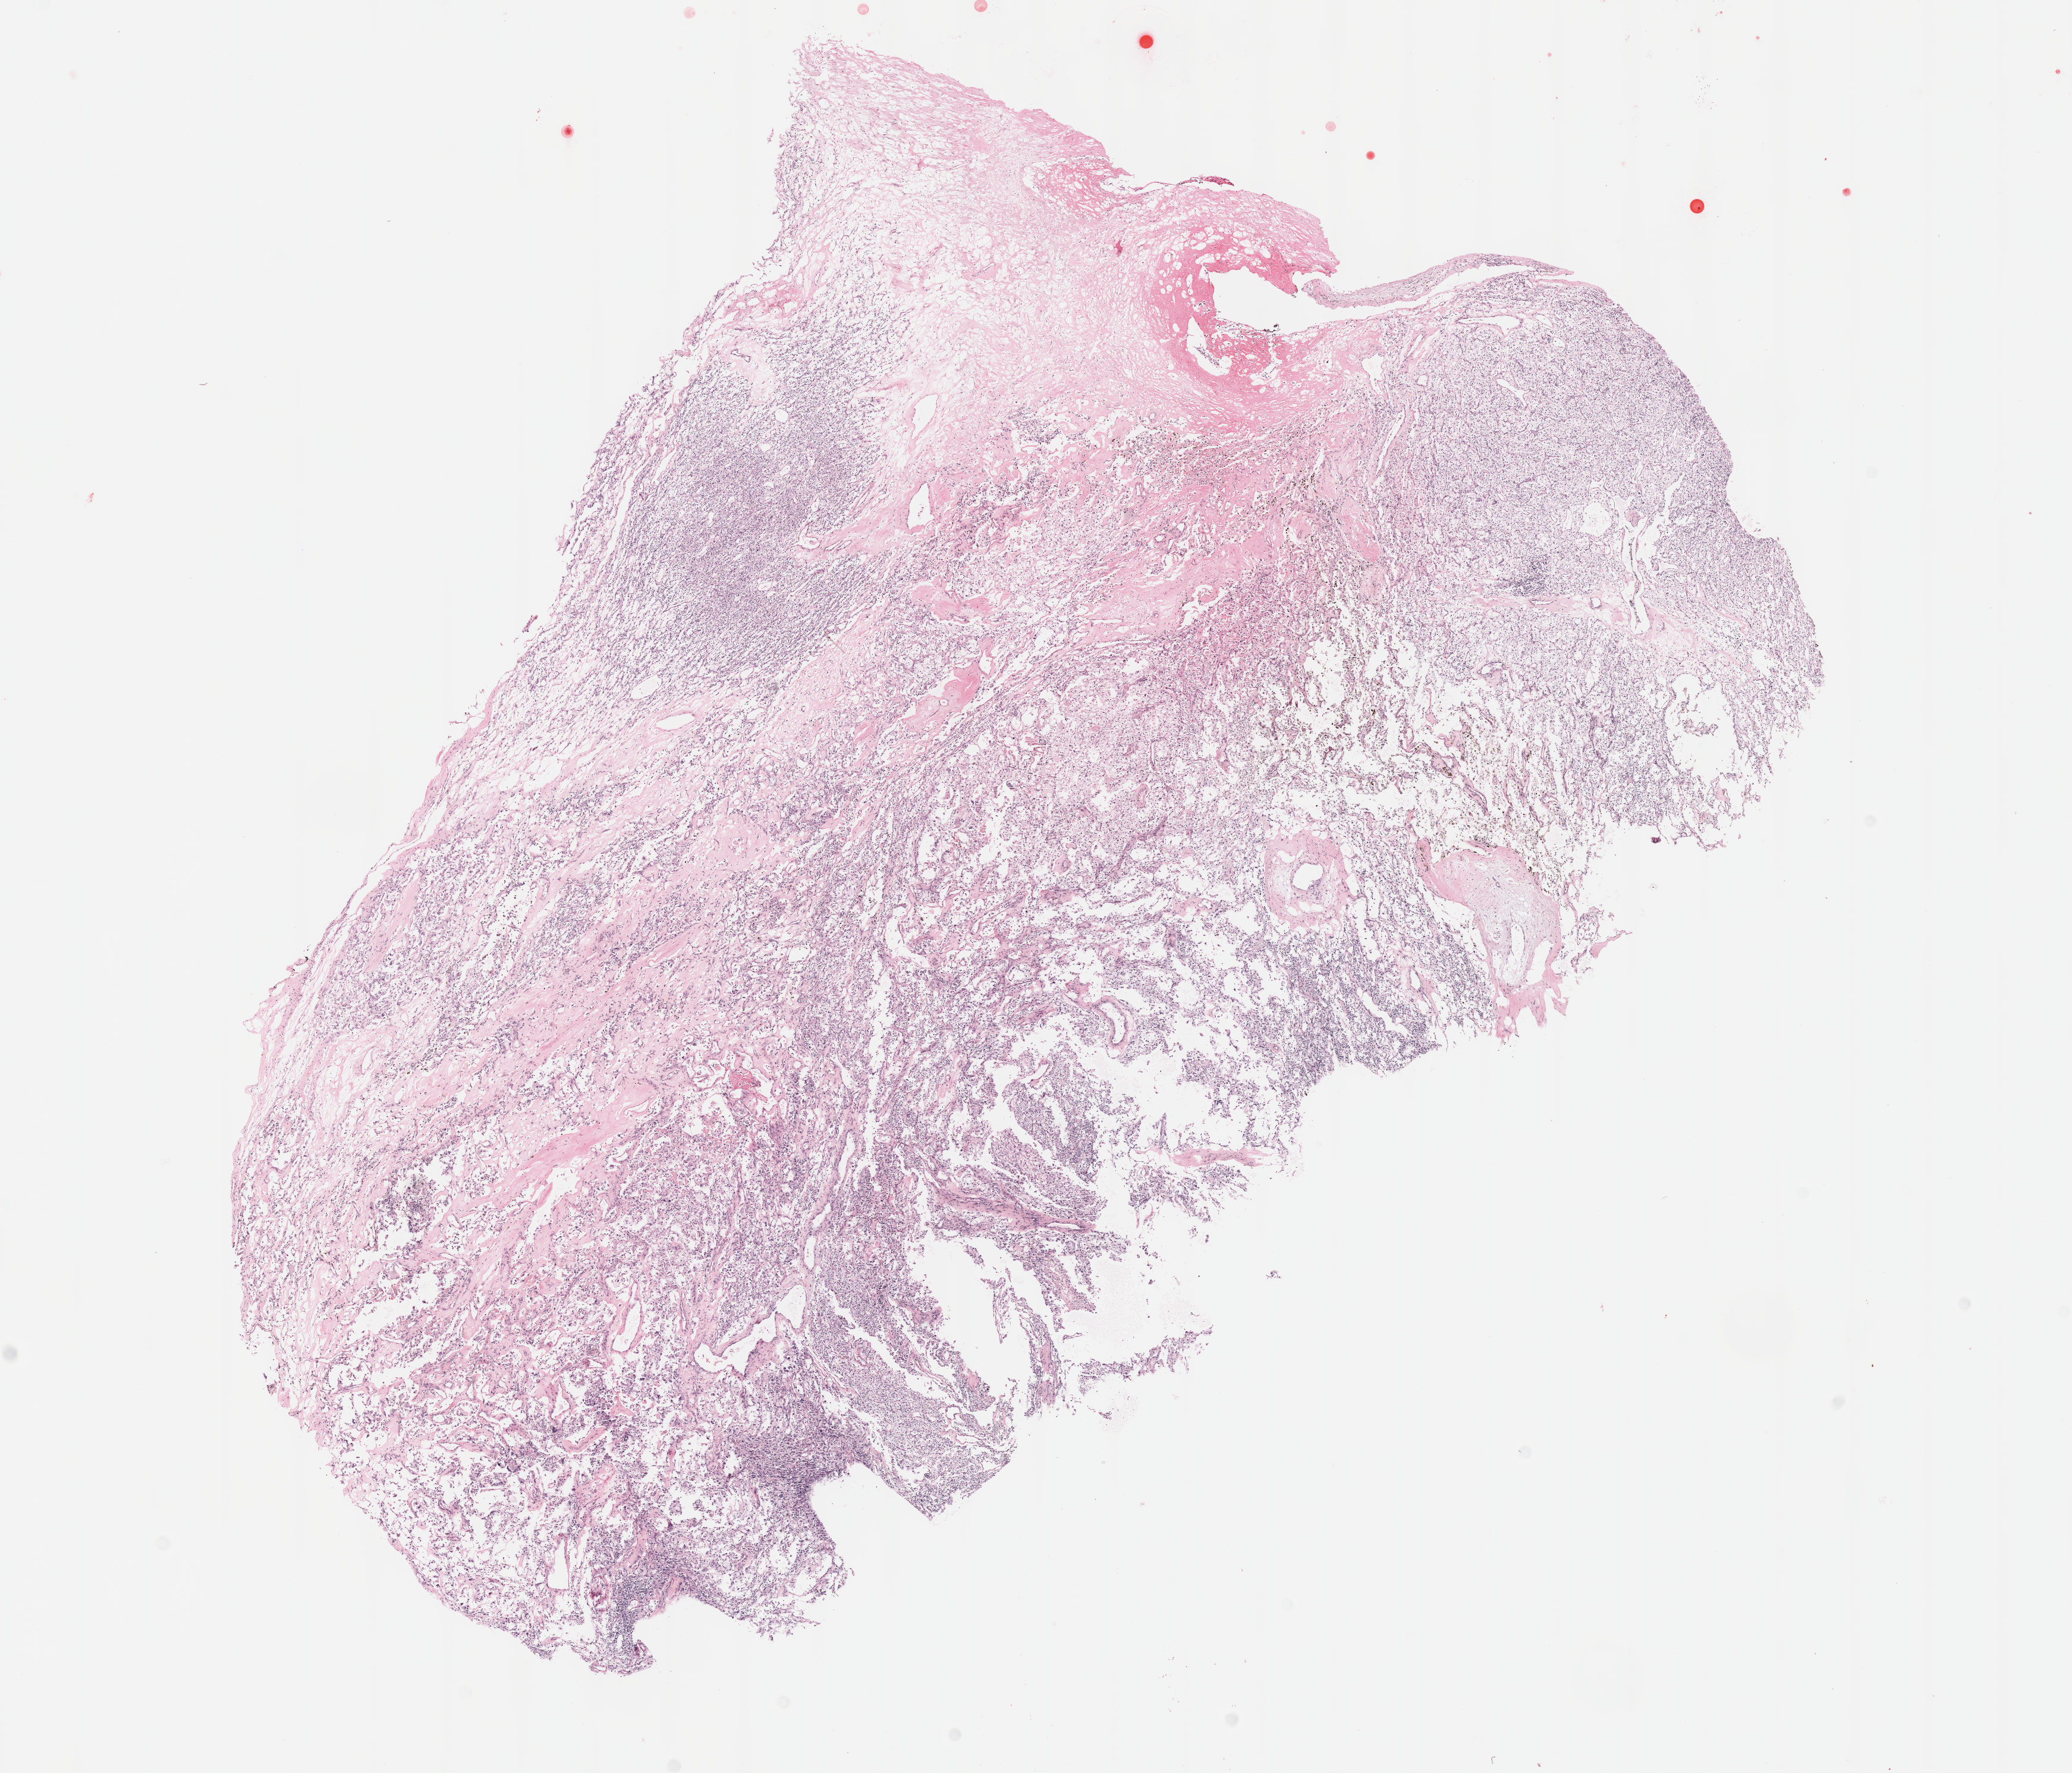
Digitized H&E tissue section (whole slide) — whole scanned area (about 14.1 x 12.1 mm) shown as a low-resolution overview. Formalin-fixed paraffin-embedded (FFPE) diagnostic section. Kidney, primary tumour sample. Male patient; age at initial diagnosis 84 years. Histologic grade: G3 (poorly differentiated).
Laterality: right. AJCC pathologic stage: I. Histologic diagnosis: Clear cell adenocarcinoma, NOS.